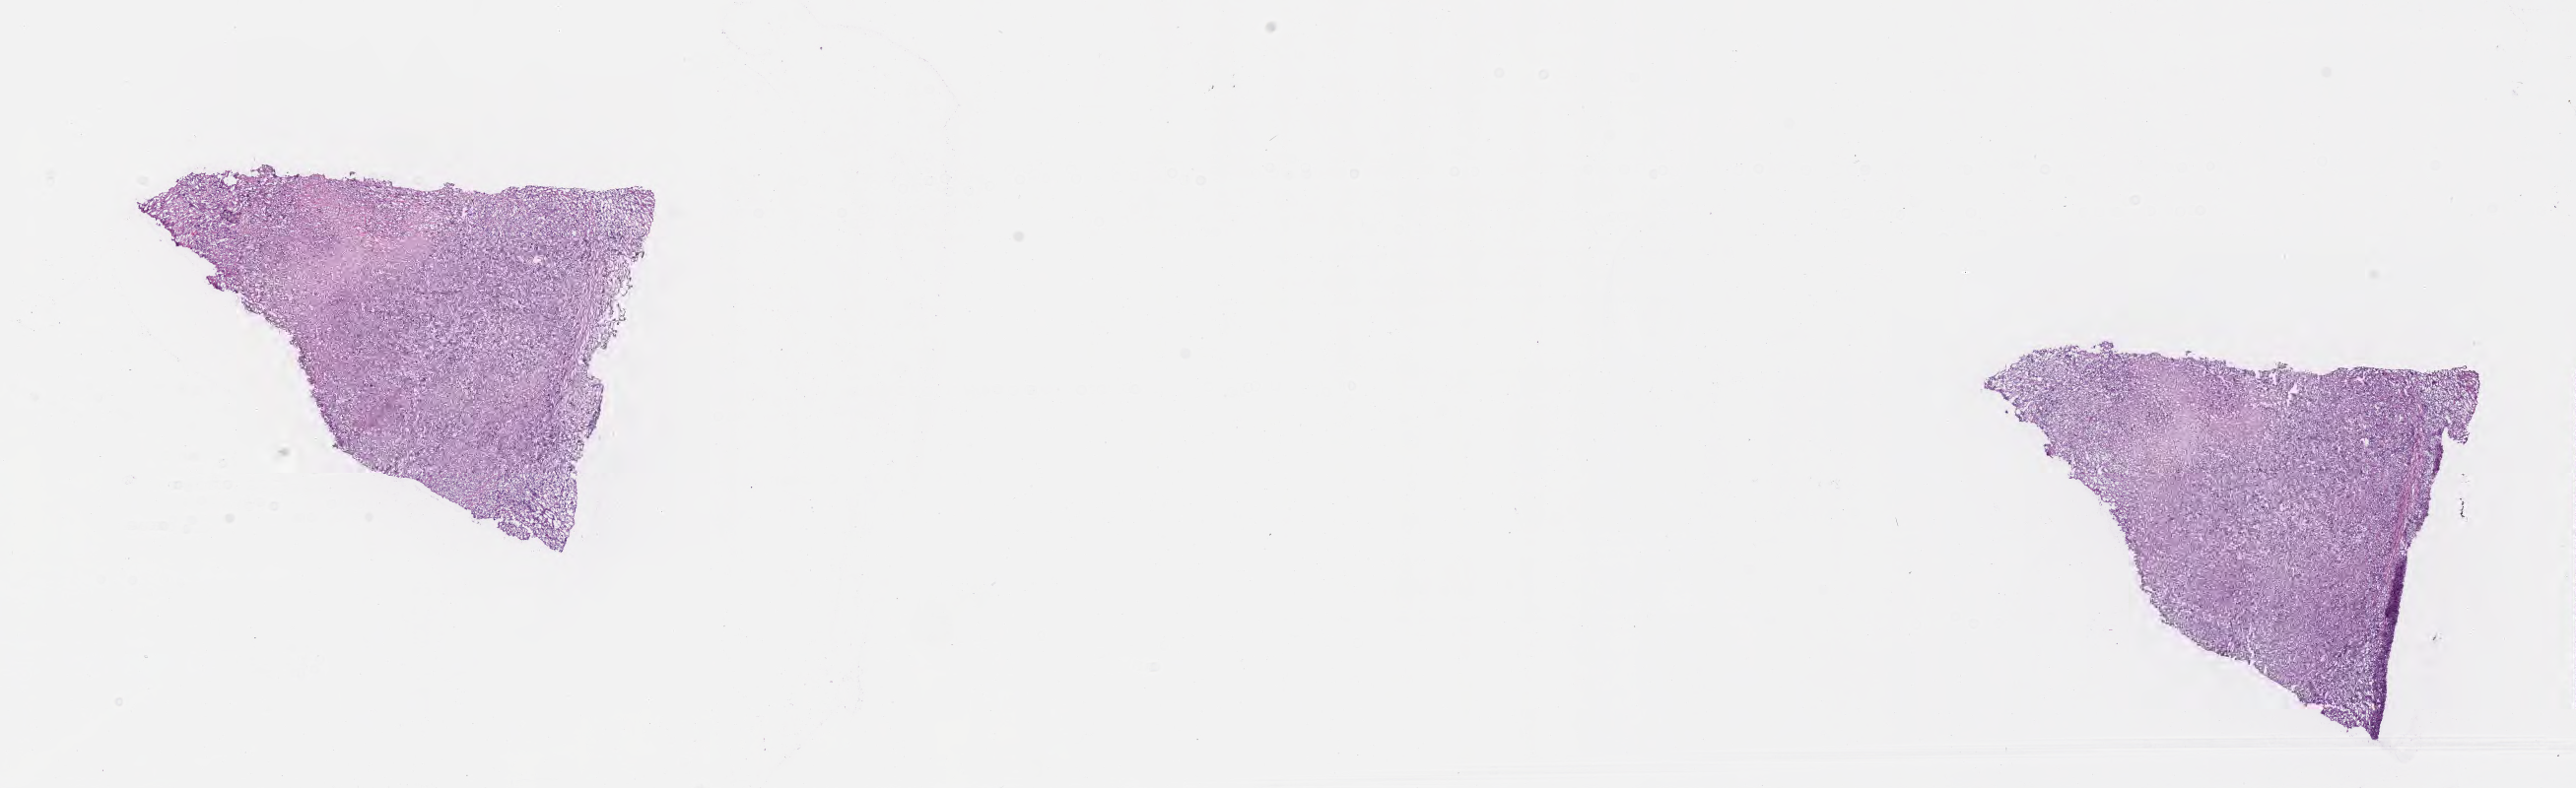
Whole-slide image, hematoxylin and eosin (H&E) stain — whole scanned area (about 21.1 x 6.5 mm) shown as a low-resolution overview. Frozen section (tissue freezing medium). Metastatic tumor tissue, resected from lymph node. Female, age 78 years at initial diagnosis. Pathologist review of this section (percent, as recorded): tumor cells 85%, tumor nuclei 85%.
Patient diagnosis (primary): Malignant melanoma, NOS.